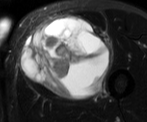
MRI of an extremity soft-tissue mass, one axial slice. Position 34 of 52 along the scan axis. T2-weighted fat-saturated. MR volume resampled by the dataset authors to the PET/CT grid (not the native acquisition matrix). 3.27 mm slice thickness. 147 × 122 image matrix, field of view 144 × 119 mm. Male patient. From the clinical record (not read from this slice): histological type: pleiomorphic liposarcoma; grade: high; site of the primary tumour: left thigh.
Annotated regions visible in this slice (expert contour drawn on MRI and transferred to this co-registered scan by the dataset authors):
- gross tumour volume including surrounding oedema: bounding box [x1, y1, x2, y2] px = [23, 16, 113, 97]
- gross tumour volume (mass): [23, 16, 111, 97]